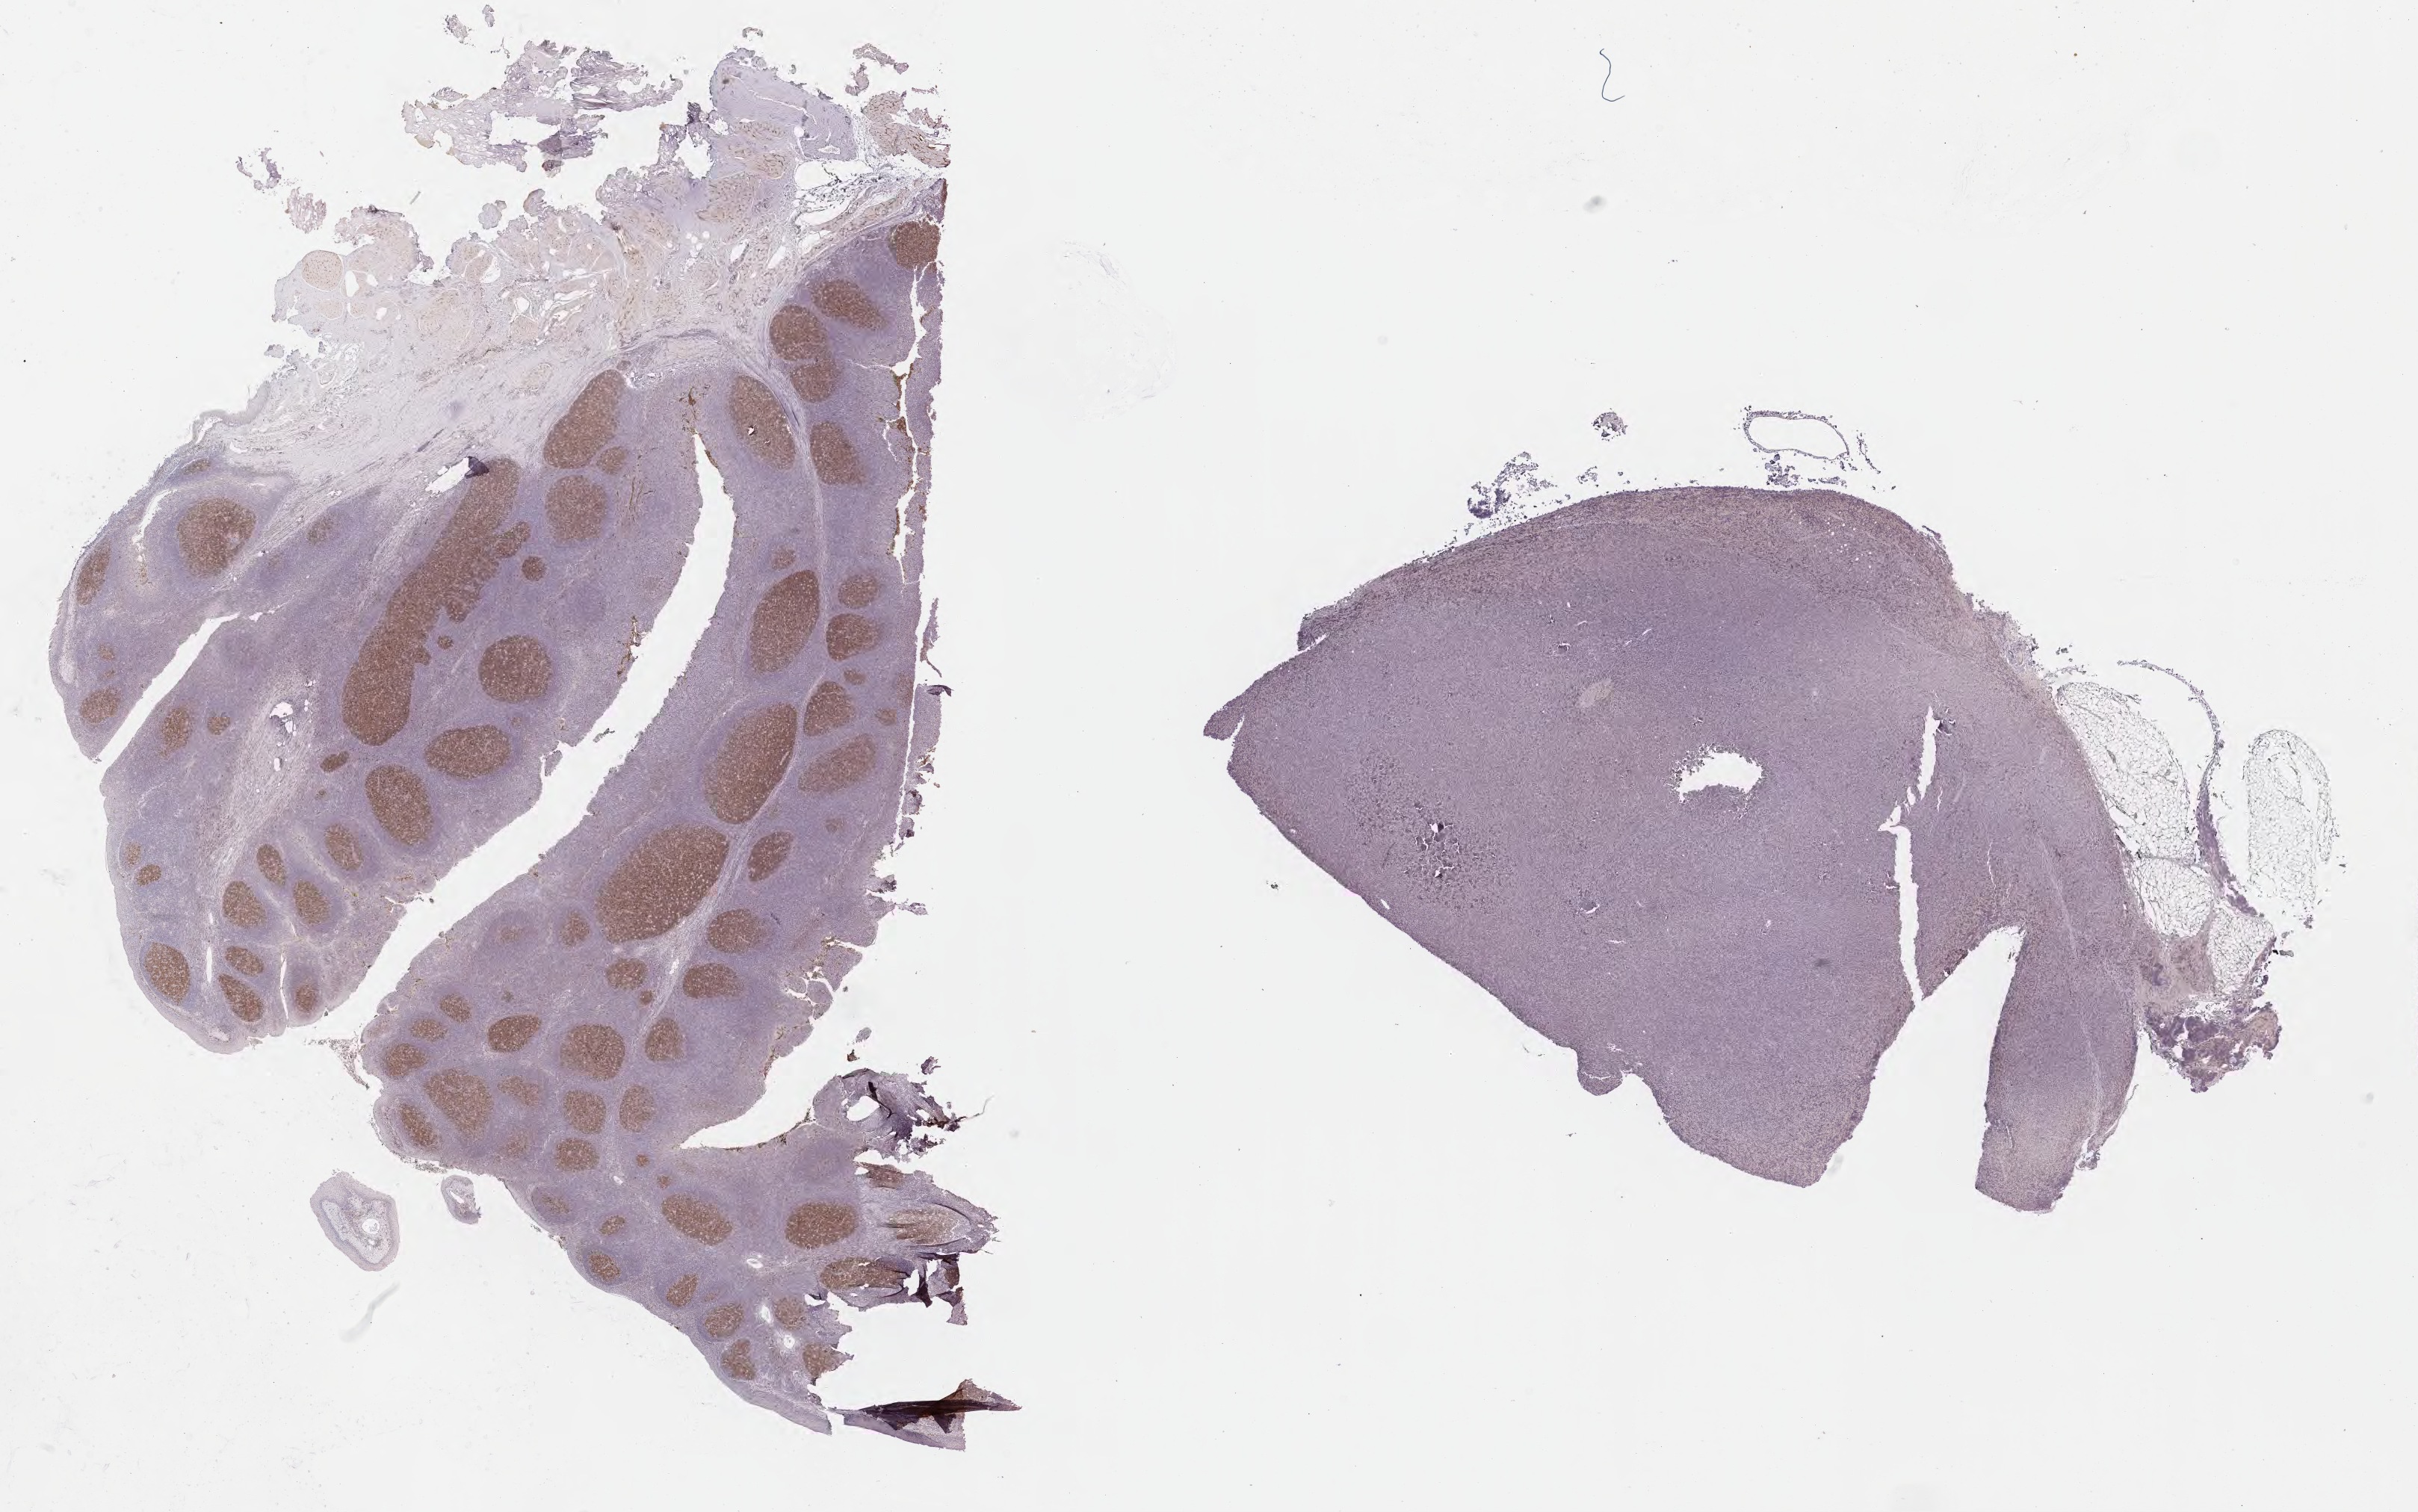
Immunohistochemistry (IHC) whole-slide image stained for CD10 — a low-resolution overview of the entire scanned area, about 26.2 x 16.4 mm, specimen: tumor tissue, site: lymph node. Patient male; aged 26.
Diagnosis: Diffuse large B-cell lymphoma, NOS.